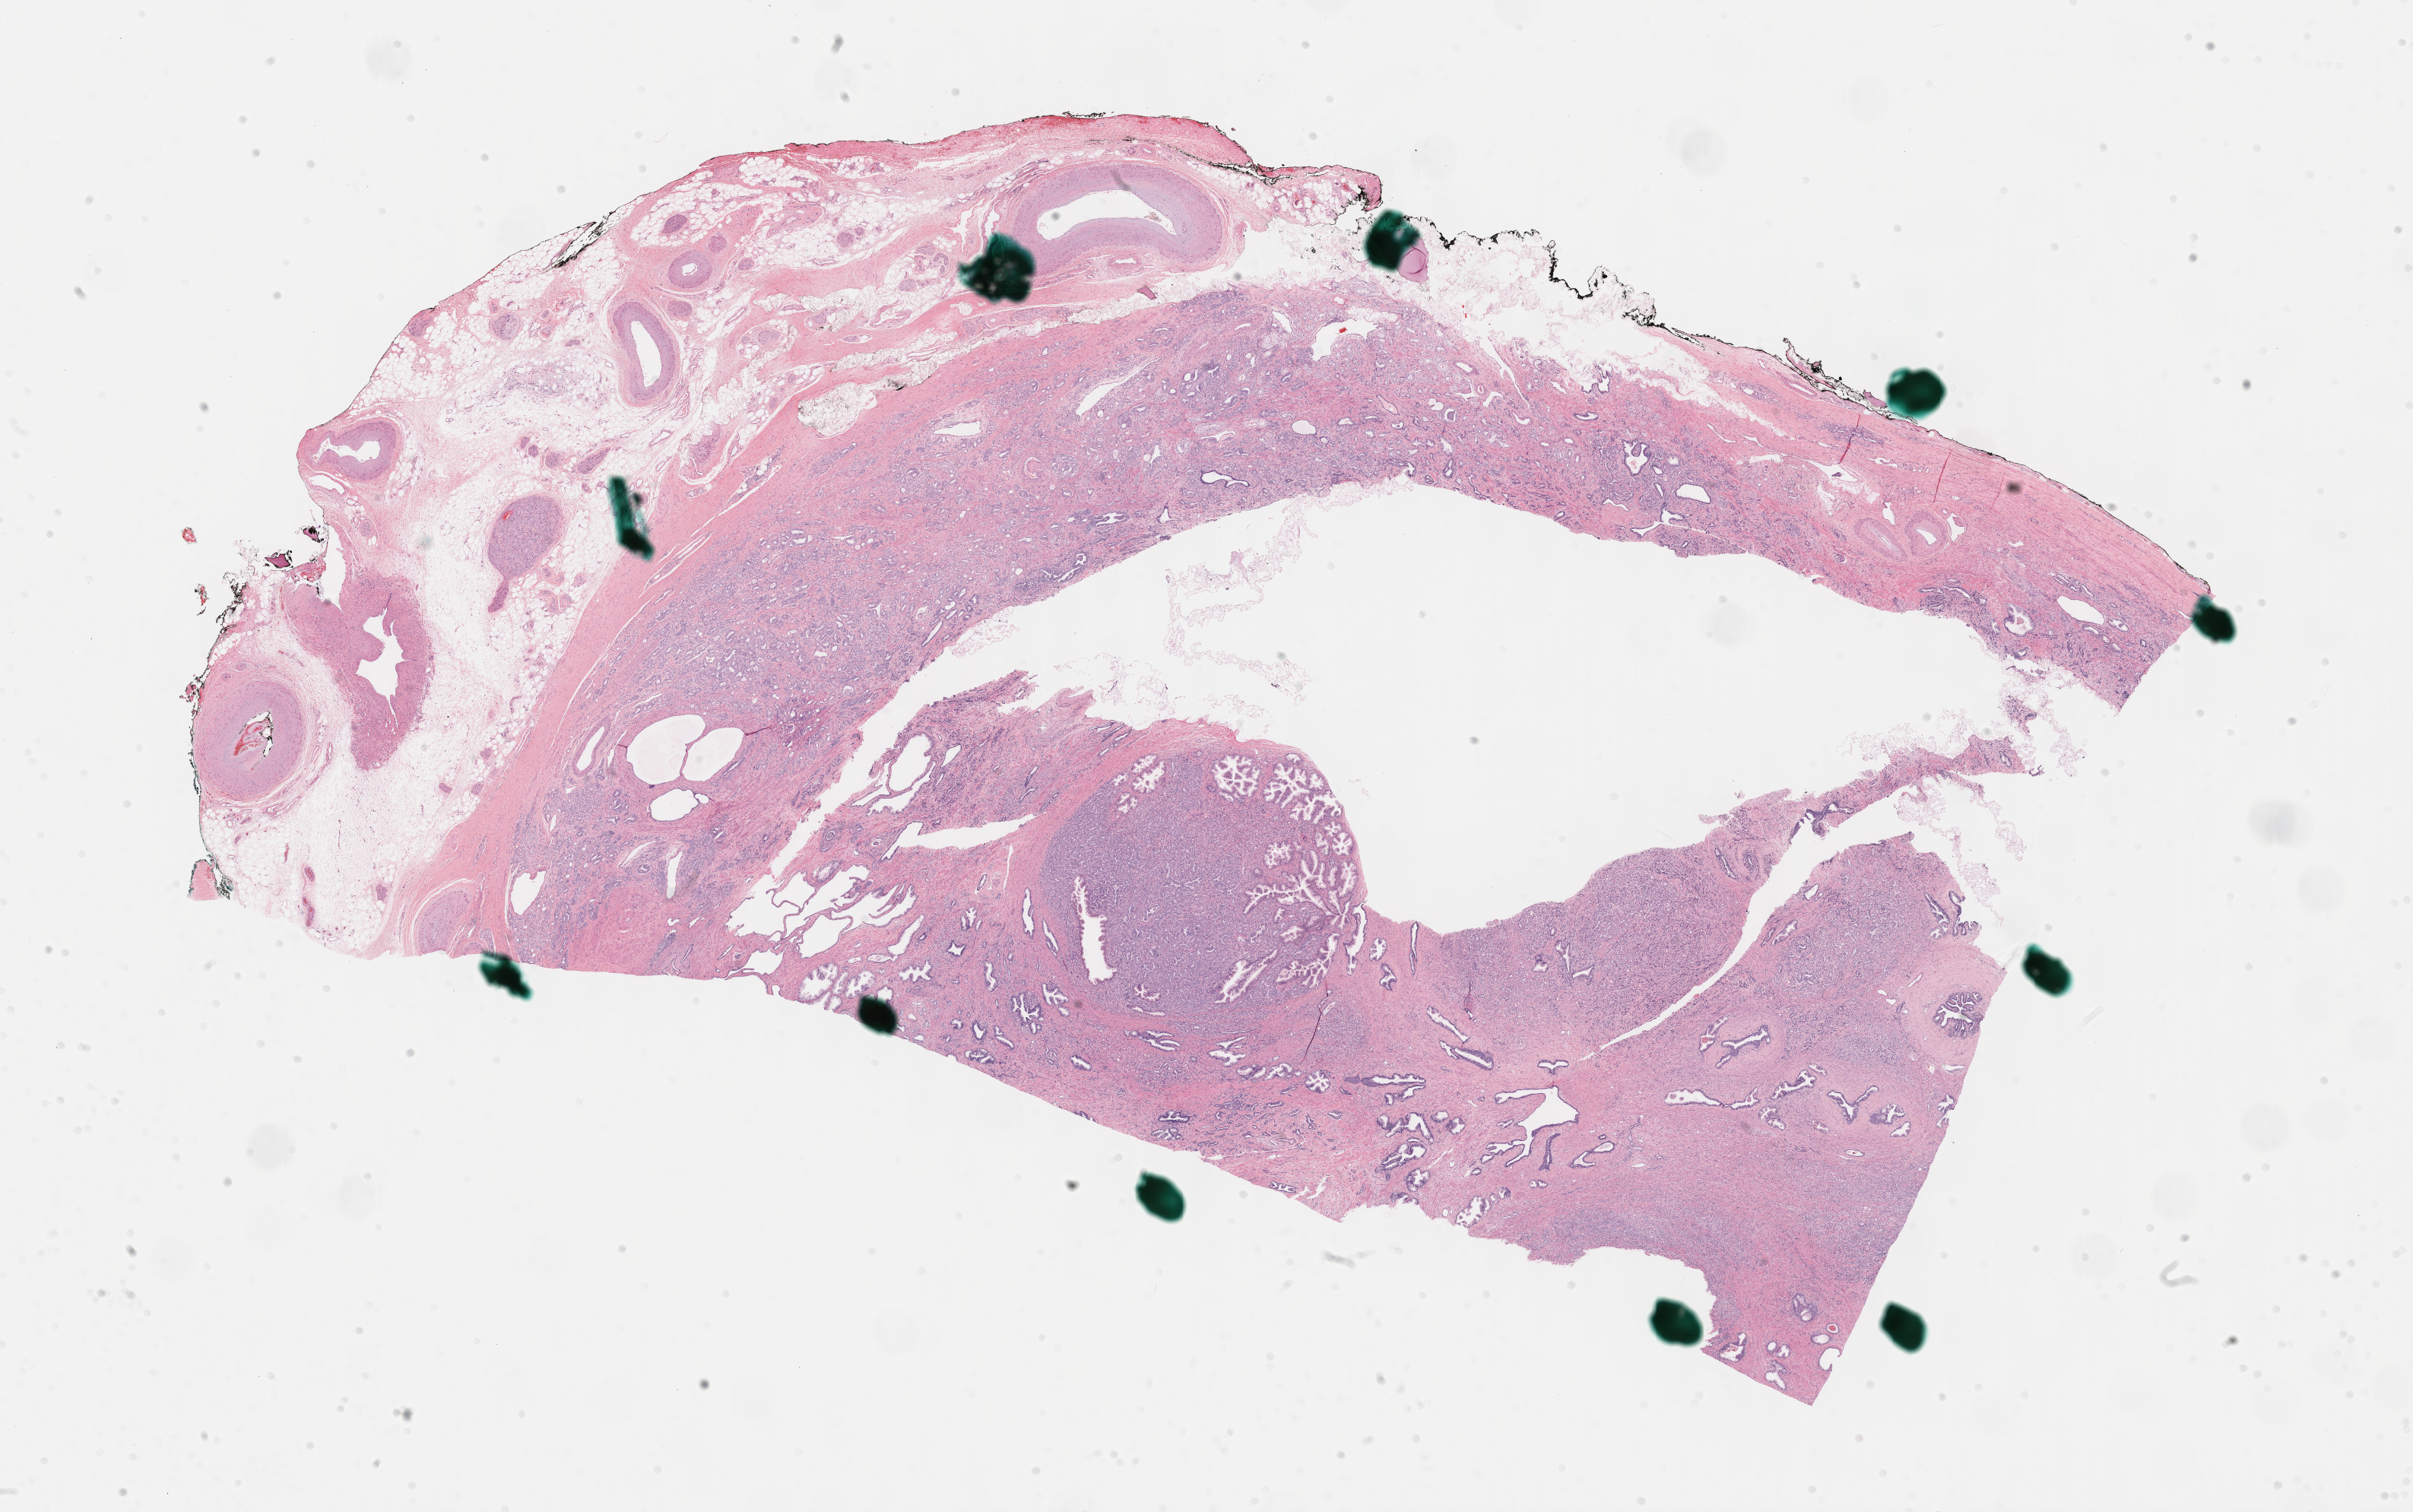
H&E-stained whole-slide image — whole scanned area (about 25.7 x 16.1 mm) shown as a low-resolution overview. FFPE section. Primary tumour sample from the prostate. Patient: male, age at initial diagnosis 53 years. Gleason score: 7 (3+4).
- histologic diagnosis: Adenocarcinoma, NOS (prostate gland)